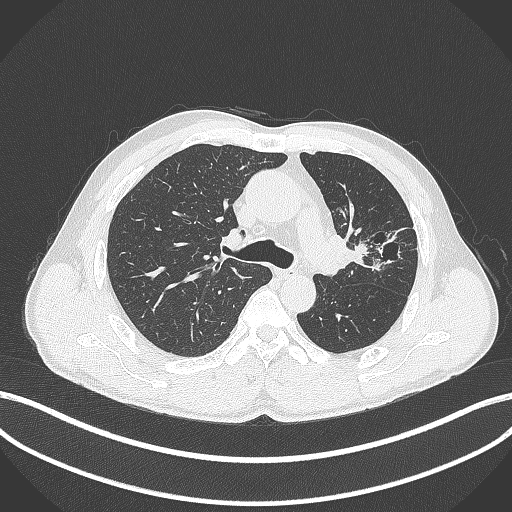
Chest CT, one axial slice; slice 275 of 429 in the series (ordered by position); lung window (W 1500 / L -600 HU); 1 mm slice thickness; 512 × 512 image matrix. Patient: male, 57 years. Case-level facts recorded for this patient, not image findings: clinical TNM (as recorded): T2b N0 M0.
Structures marked on this image (bounding box drawn by a radiologist):
- lung tumour (recorded histology: squamous cell carcinoma): bounding box [x1, y1, x2, y2] px = [333, 232, 384, 272]